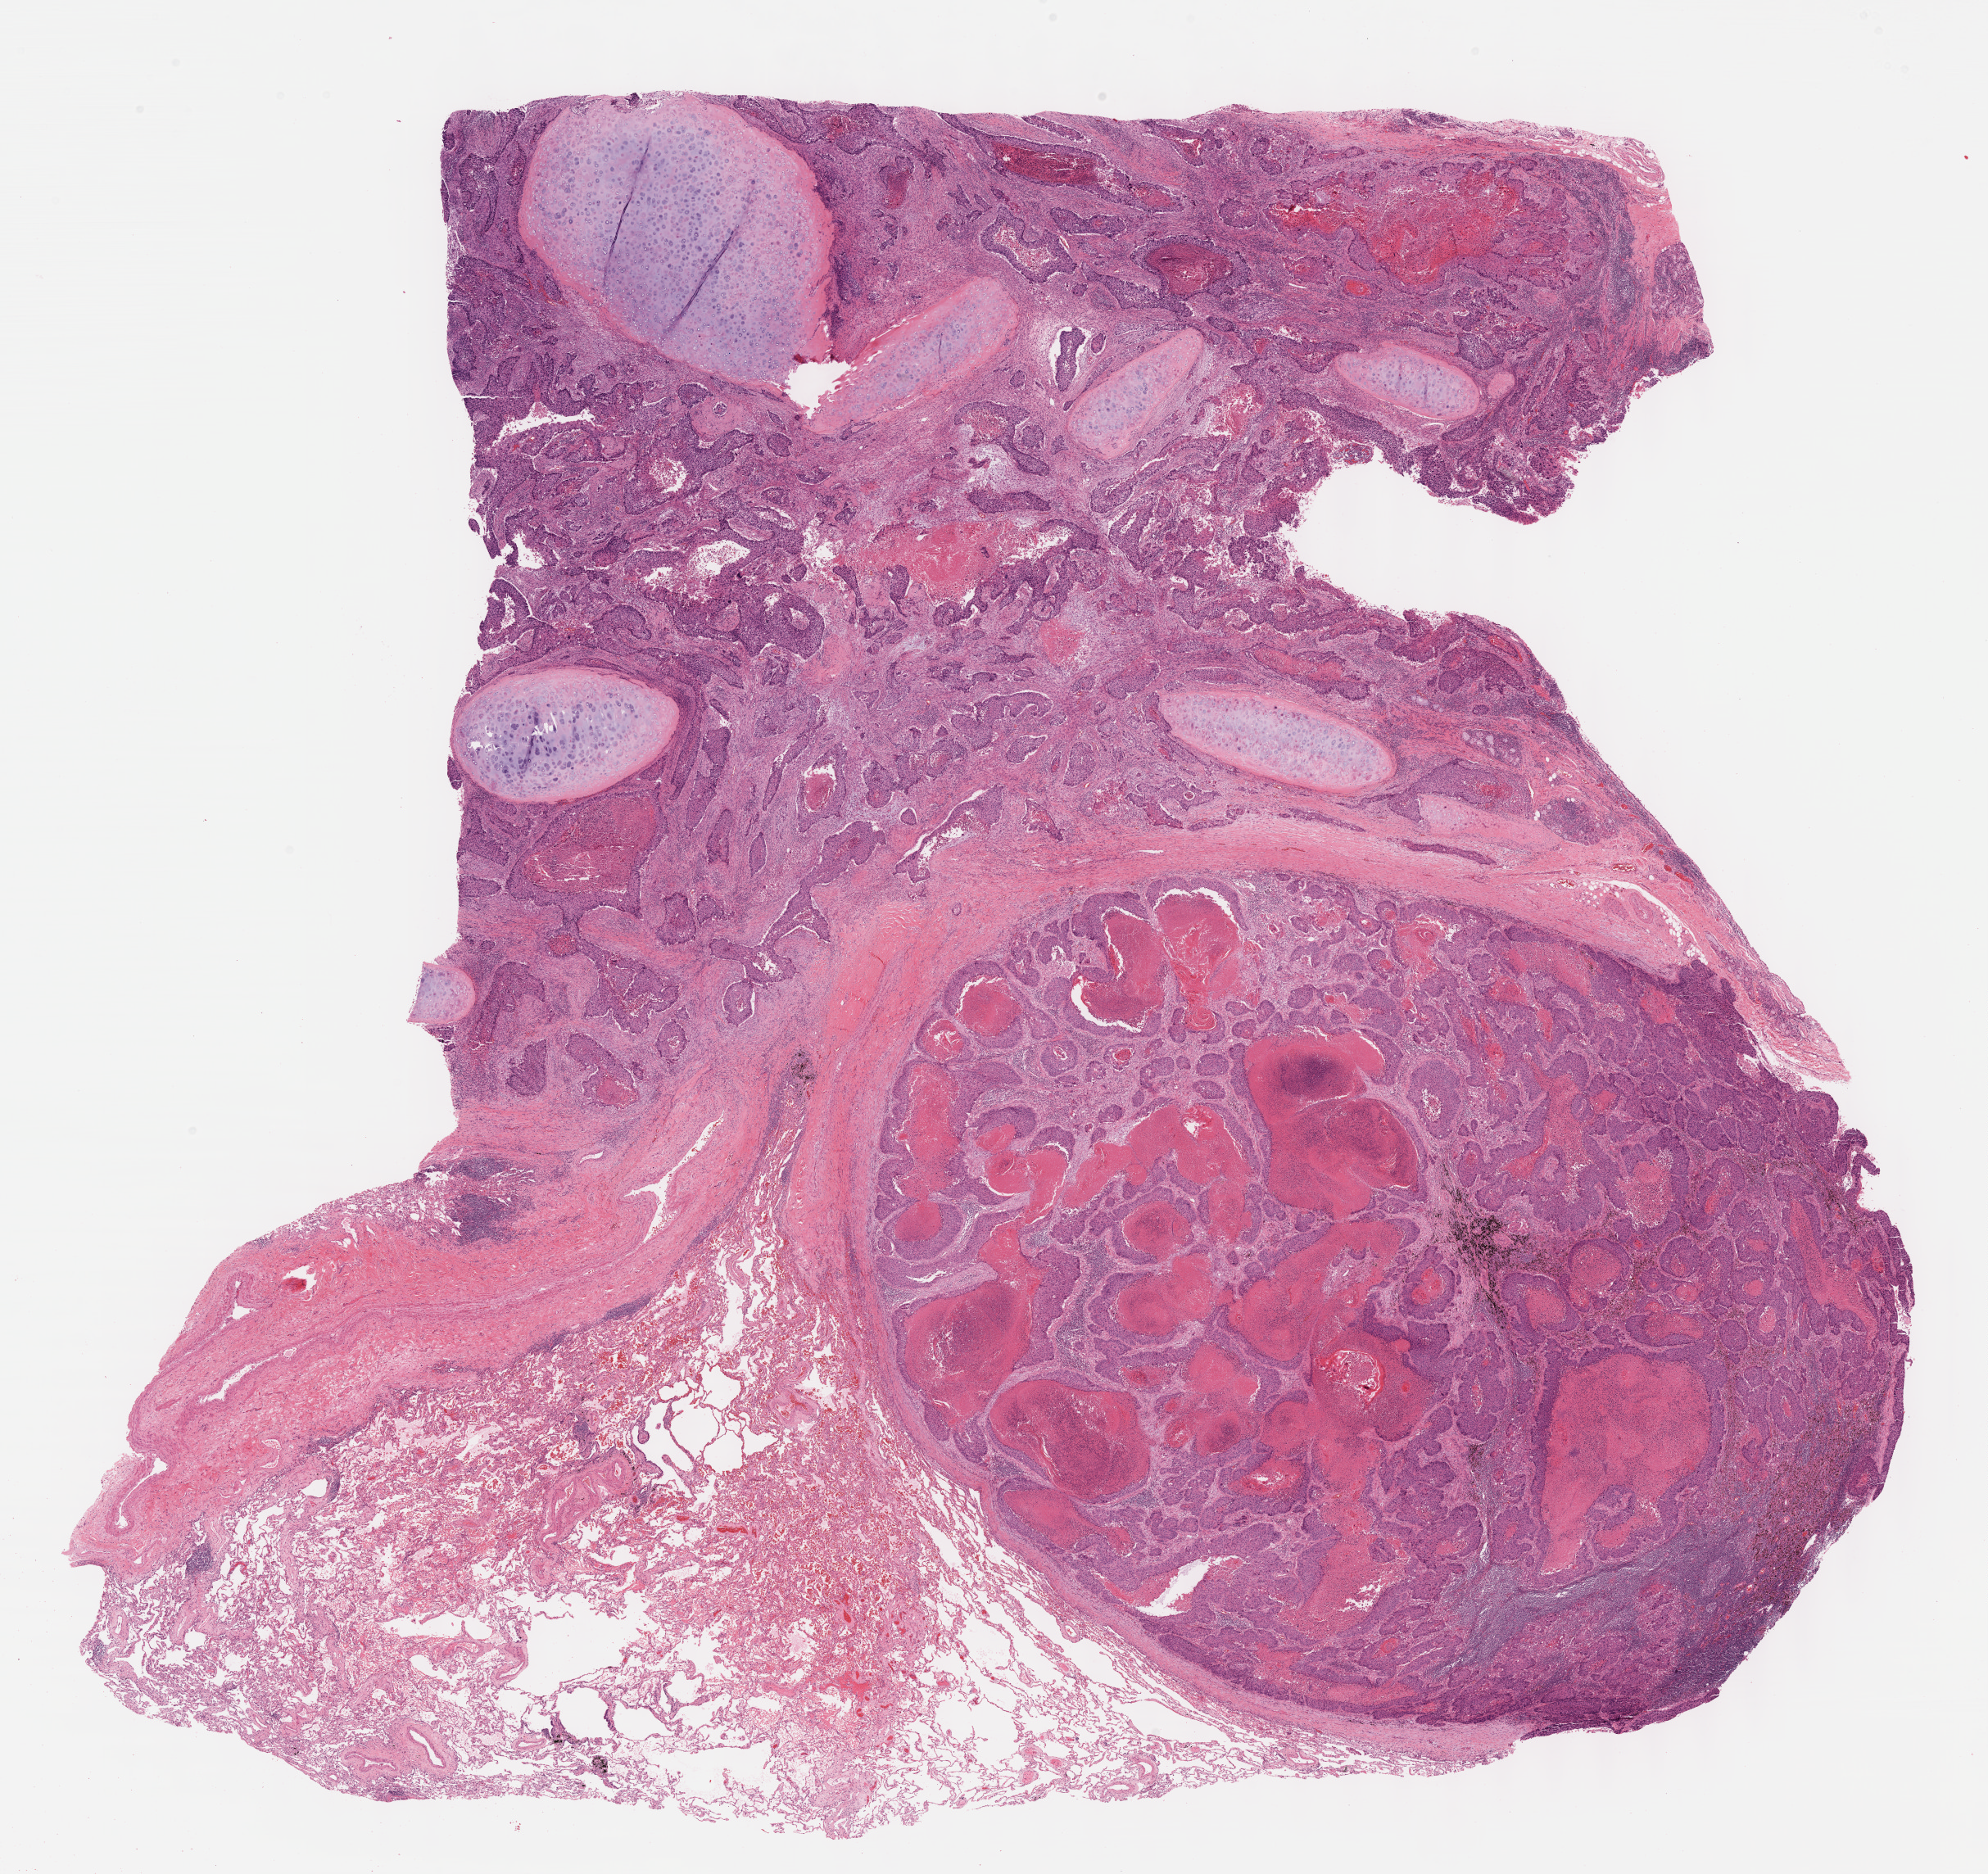
Whole-slide histology image, H&E — a low-resolution overview of the entire scanned area, about 19.6 x 18.5 mm (from a 40x scan), formalin-fixed paraffin-embedded (FFPE) diagnostic section, sample: primary tumour, lung. Patient: female, age at initial diagnosis 60 years.
Pathologic diagnosis: Squamous cell carcinoma, NOS (lower lobe, lung).